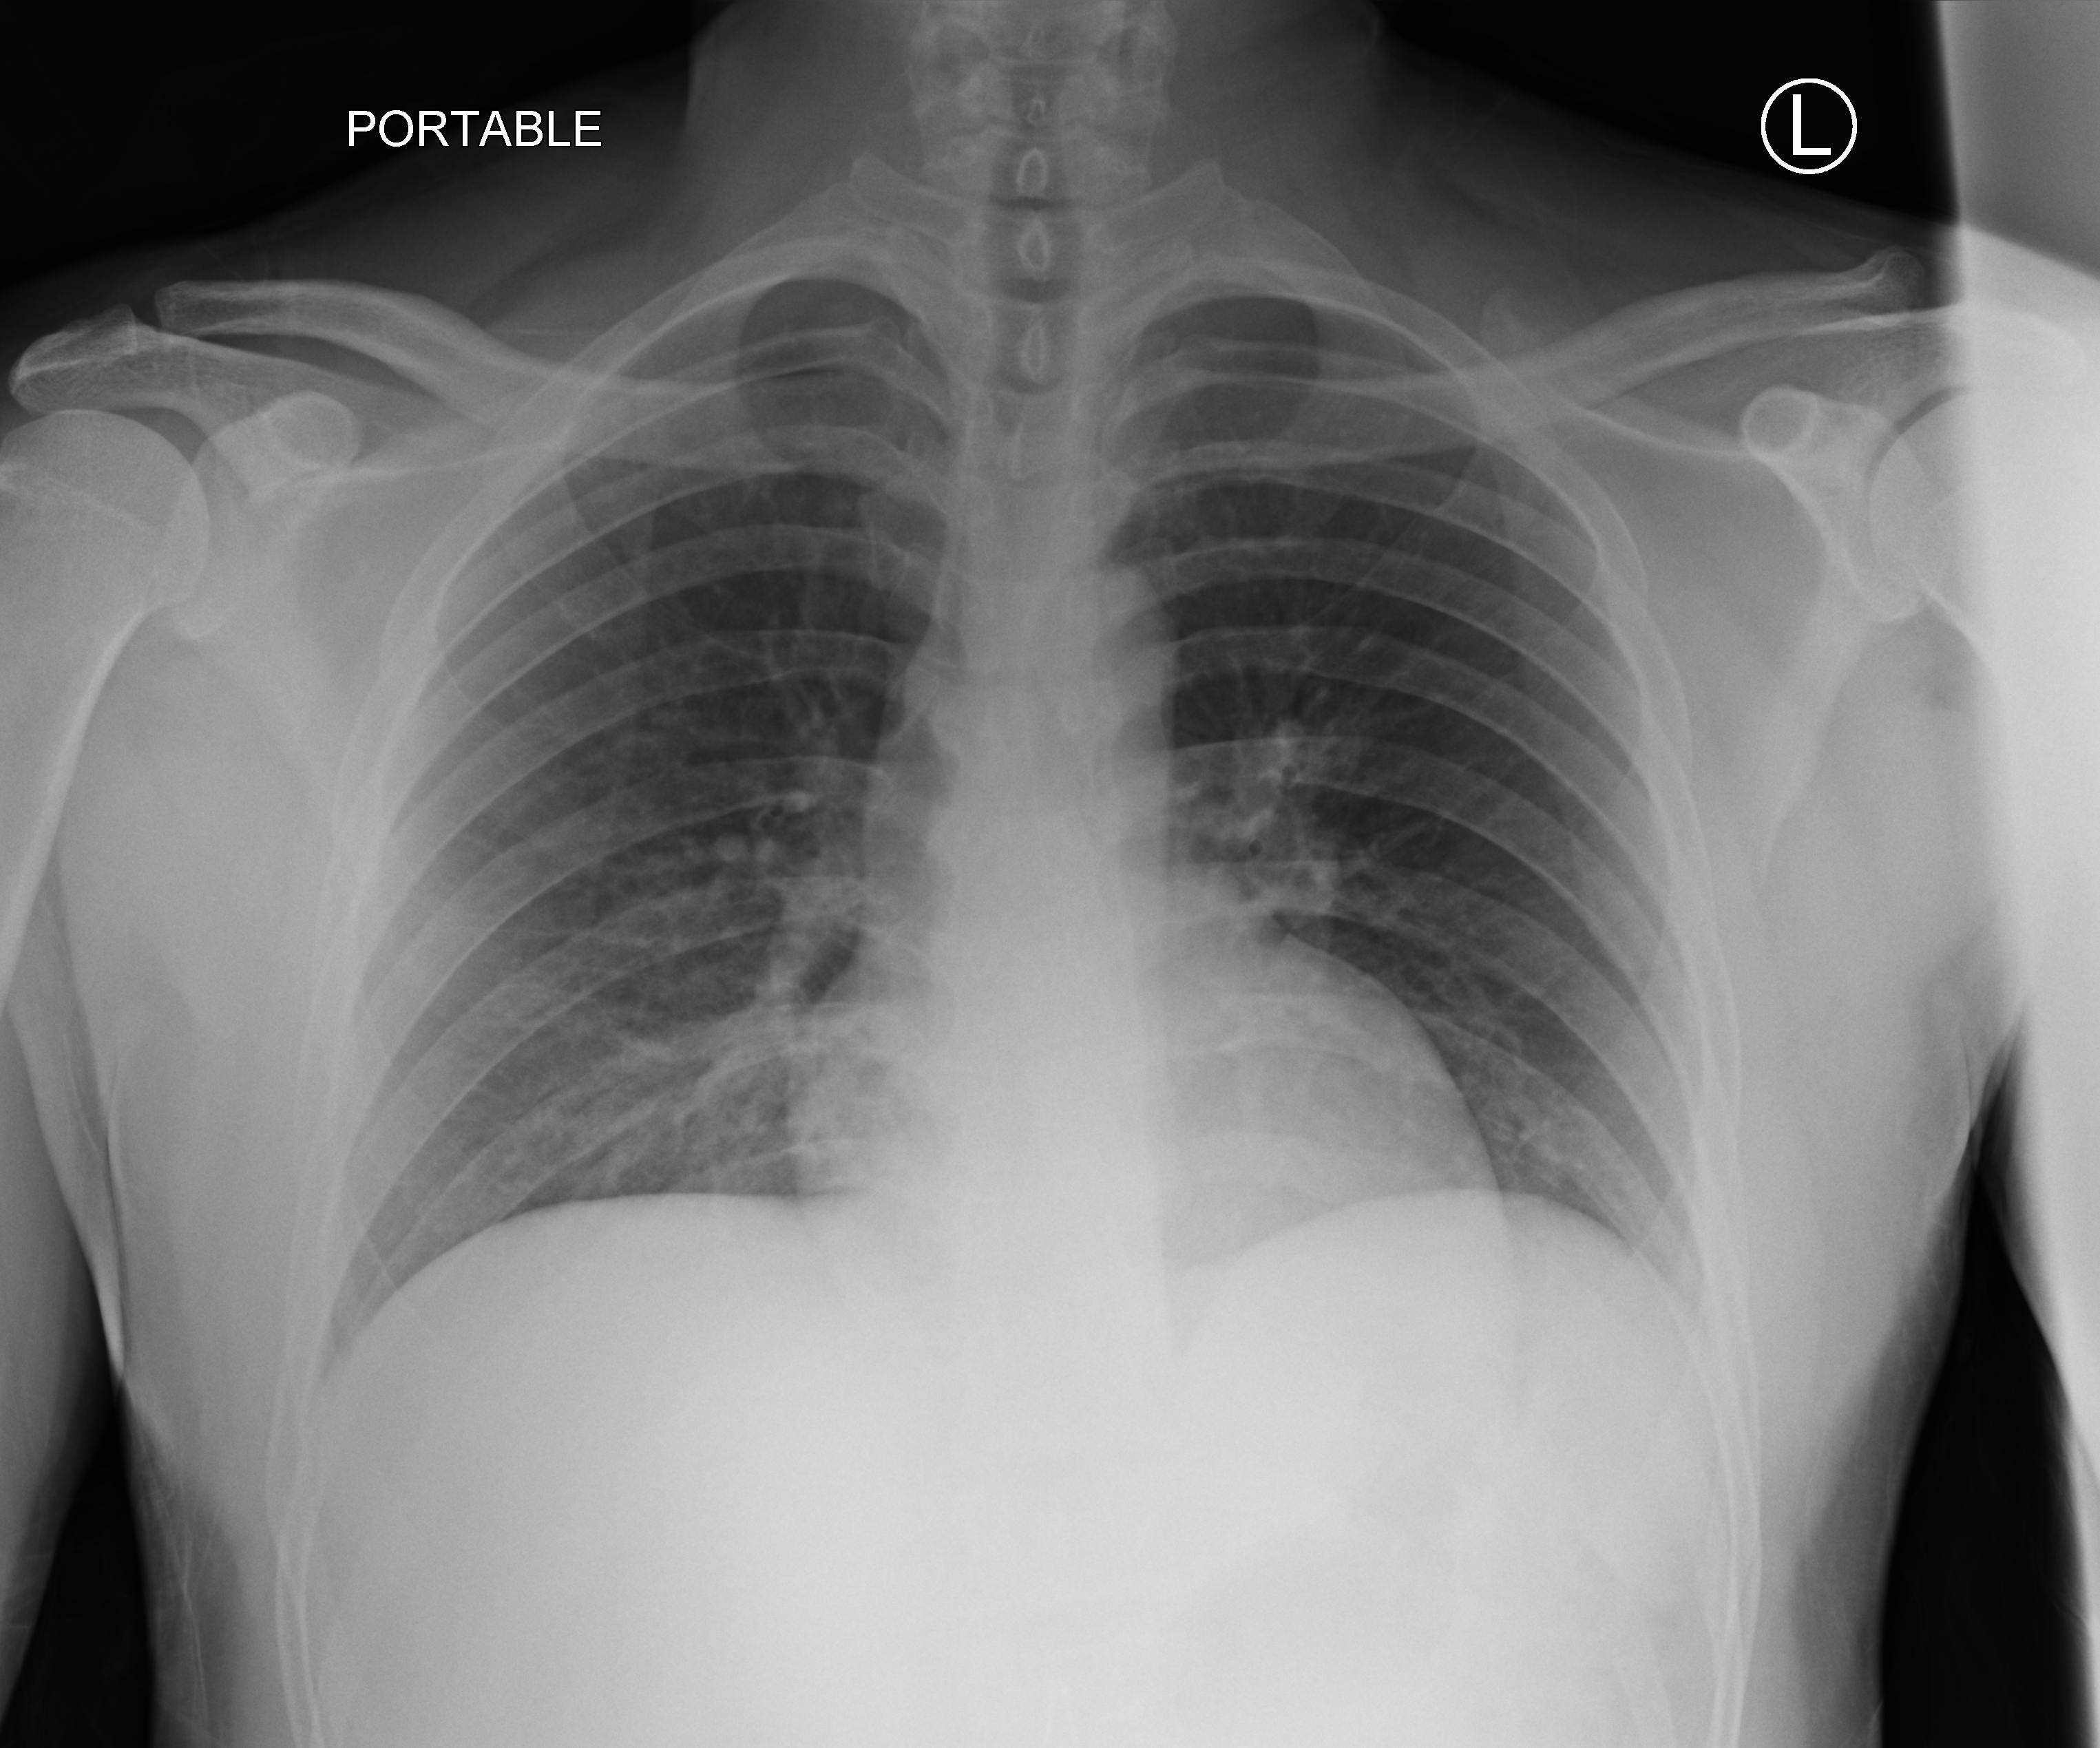
Bedside chest radiograph (computed radiography); anteroposterior (AP) projection. Male patient hospitalised with COVID-19, age 18–59 years.
From the hospital-stay record, not from the radiograph (when in the stay this image was taken is not recorded): length of hospital stay: 2 days; admitted to intensive care during this hospital stay: no; mechanically ventilated during this hospital stay: no.